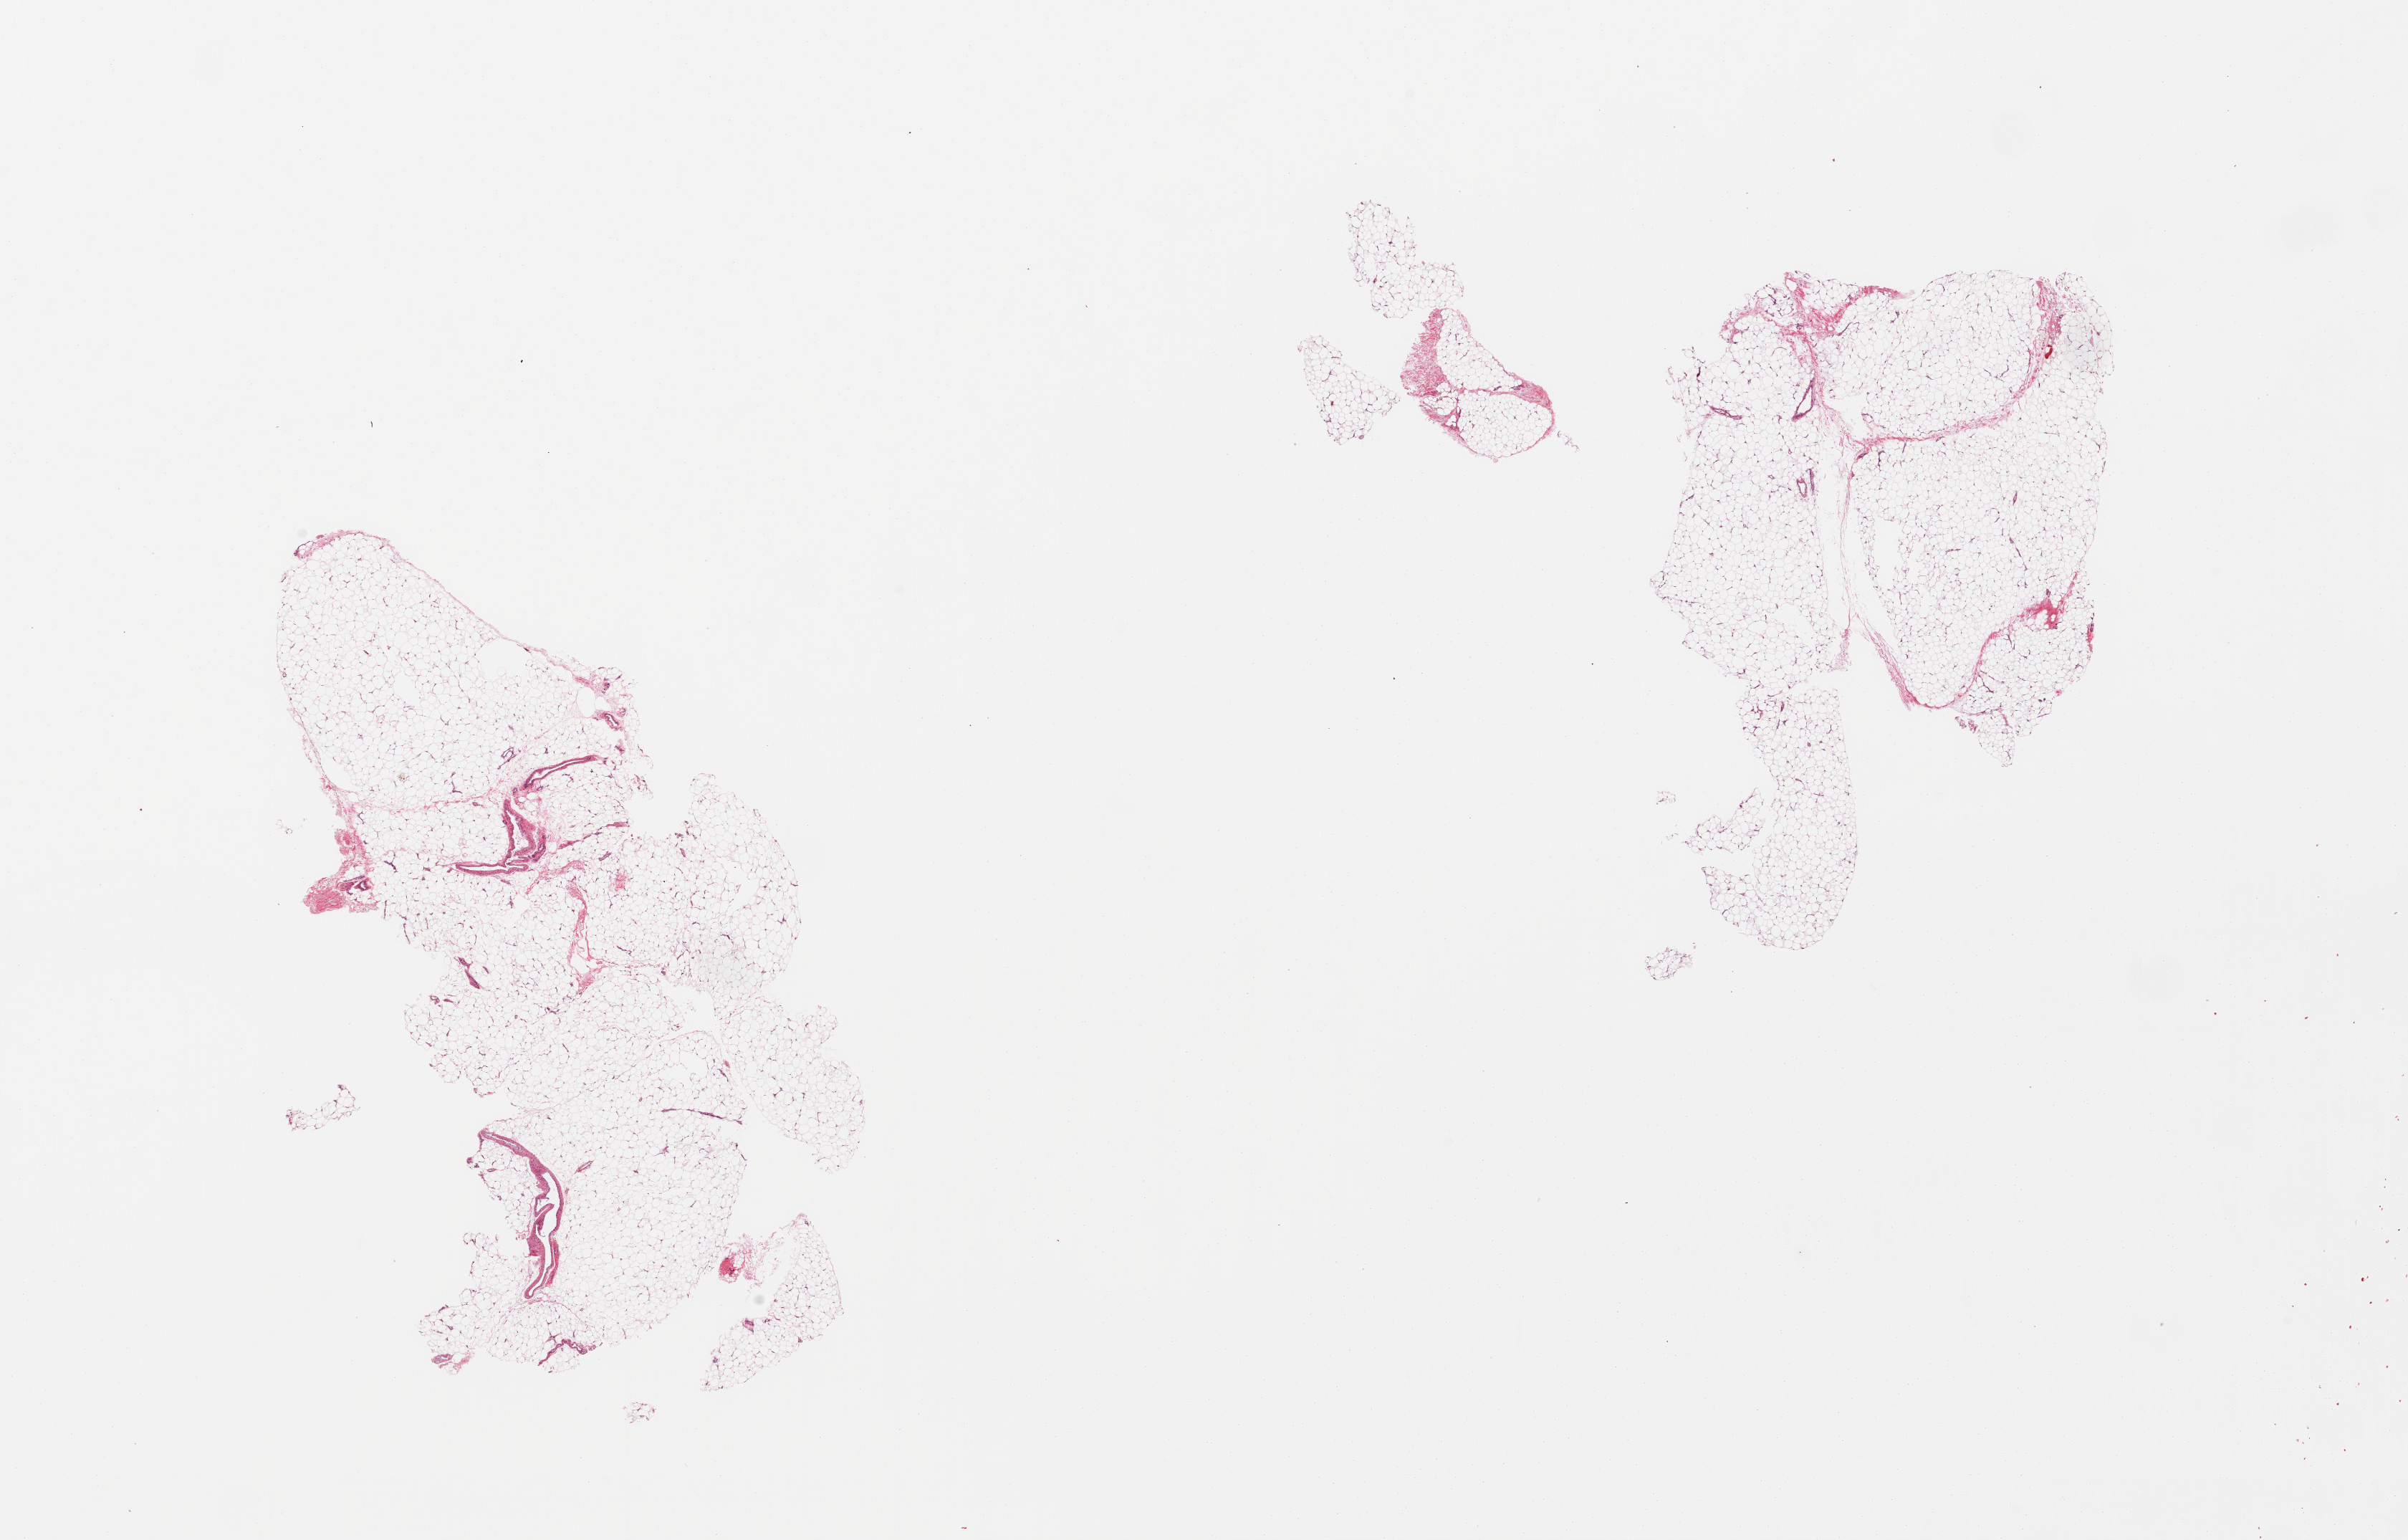
Whole-slide image, hematoxylin and eosin (H&E) stain — low-resolution overview of the scanned area, about 26.6 x 17.0 mm. PAXgene-fixed paraffin-embedded (PFPE) section. Section of adipose tissue (target tissue). Tissue donor sample. Donor sex: female.
Pathologist's review note for this sample: 2 pieces.